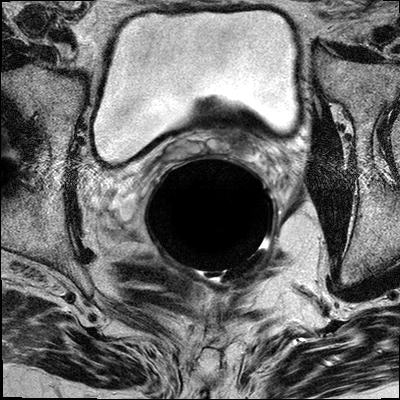
Prostate MRI examination; 3 images, each a single mid-volume slice chosen by position (not for content). Treatment context recorded for this patient: Surgery.
Image 1: T2-weighted axial slice, series "T2W_TSE_AX", slice 17 of 32.
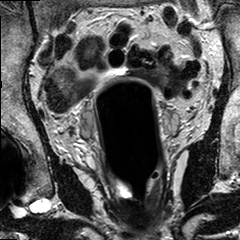
Image 2: coronal T2-weighted image, slice 13 of 24.
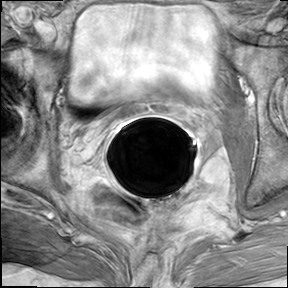
Image 3: DCE (dynamic gadolinium-enhanced) axial slice, series "AX BLISS_GAD_8", slice 17 of 32, dynamic phase 5 of 8, 6 mm slice thickness.
Radiologist's MRI report for this examination:
FINDINGS: The prostate has a maximal lateral diameter of 4.7 cm, a maximal craniocaudal diameter of 3.4 cm and a maximal AP diameter of 3.1 cm resulting in an estimated gland volume of 29.7 cc. The zonal anatomy is preserved. In the left peripheral zone involving all 3 levels of the prostate (base, mid third and apex), between 2;00 and 7:00, with involvement of the paramedian right peripheral zone there is a homogeneously hypointense geographic area seen (maximal extension of dominant tumor in the axial plane is 2.8 x 1.2 cm), which shows suspicious wash-in and wash-out kinetics on the dynamic series. The pseudocapsule adjacent to the left neural vascular bundle is irregular and thickened and there is suspicious enhancement seen within the pseudocapsule and with a radial extension of 1 mm there are several small areas of suspicious enhancement extending beyond the pseudocapsule at the left prostate base. In the left apex the tumor reaches the gland borders periurethral. No evidence for involvement of the right neurovascular bundle. No evidence for seminal vesicles infiltration; the tumor reaches up to the left seminal vesicle base, without evidence of direct infiltration. No evidence of involvement of bladder neck and rectal wall. No suspiciously enlarged obturator and iliac lymph nodes (up to the aortic bifurcation). Incidental note is made of diverticulosis. IMPRESSION: Prostate cancer within the left peripheral zone, and to a lesser extent in the paramedian right peripheral zone, involving all three levels of the prostate. Findings are suspicious for beginning extraprostatic extension at the base towards the left neurovascular bundle. (radial extension 1 mm). At the left apex the tumor reaches the gland borders, at the base the tumor reaches the left seminal vesicles base. No without evidence of direct infiltration of seminal vesicles on either side. No evidence of right neurovascular bundle involvement. No evidence of rectal wall or urinary bladder involvement. No pelvic lymphadenopathy.

Prostatectomy specimen pathology (as recorded; the surgery followed this MRI):
Gross Description
The specimens are received in three containers labeled with the patient' s name, hospital number and A. "Left Pelvic Lymph Nodes", B. "Right Pelvic Lymph Nodes" and C. "Prostate Gland".
Specimen A consists of a 4.5x2x0.5 cm single whole fatty lymph node with minimally attached fibroadipose tissue. The lymph node is serially sectioned and the entire specimen is submitted in cassettes as follows: A1 and A2 fatty lymph node, serially sectioned, A3 remaining fibrofatty tissue. Specimen B consists of a 4x2x05. cm piece of fibrofatty tissue from a single whole lymph node dissected which measures 2.5 cm. The entire specimen is submitted in cassettes as follows: B1 and B2 single whole lymph node, serially sectioned, B3 remaining fibrofatty tissue. Specimen C consists of a 42.9 grams, 4x3x2.8 cm radical prostatectomy specimen with bilateral attached vas and seminal vesicles. The right and left seminal vesicles average 4x1.5x0.4 cm, right and left vas average 3.5 cm in length by 0.3 cm in diameter. The specimen is inked as follows: right side black, left side blue. Proximal and distal margins are taken enface and radially sectioned. The specimen is serially sectioned to reveal a 3x2 cm pale-white, hard mass present in the right posterior and left posterior lobe which grossly abuts the overlying inked margin. There is focal cystic present in the left anterior lobe. Representative sections are submitted in cassettes as follows: C1 and C2 radial section, distal urethral margin, C3 and C4 radial section, proximal bladder base margin, C5 right seminal vesicle and right vas, C6 left seminal vesicle and left vas, C7 thru C10 right anterior lobe, inferior to superior, C11 thru C14 right posterior lobe, inferior to superior, C15 thru C18 left posterior lobe, inferior to superior, C19 thru C22 left anterior lobe, inferior to superior. Procedure: Radical Prostatectomy Prostate Size: 4x3x2.8cm. Weight: 42.9g grams Lymph Node Sampling: Pelvic lymph node dissection Histologic Type: Adenocarcinoma (acinar, not otherwise specified) Gleason Score Primary Pattern: 4 Secondary Pattern: 4 Total Gleason Score: 4+4=8/10 Tertiary pattern: 3 (Approximately 15% of the tumor volume) Tumor Quantitation / Proportion of prostate involved by tumor: Approximately 65% Extraprostatic Extension: Present Specify sites: Left posterior and lateral Seminal Vesicle Invasion: Not identified Margins: Margins involved by invasive carcinoma Specify sites: Multifocal, Left posterior and lateral margin Treatment Effect on Carcinoma: Not identified Lymph-Vascular Invasion: Not identified Perineural Invasion: Present Additional Pathologic Findings: Chronic Inflammation AJCC Pathologic Staging (7th ed.): (pT3a, pN0, pMx) pT3a: Extraprostatic extension or microscopic invasion of bladder neck pN0: No regional lymph node metastasis Specify: Number examined: 2 Number involved: 0 pMx Not applicable